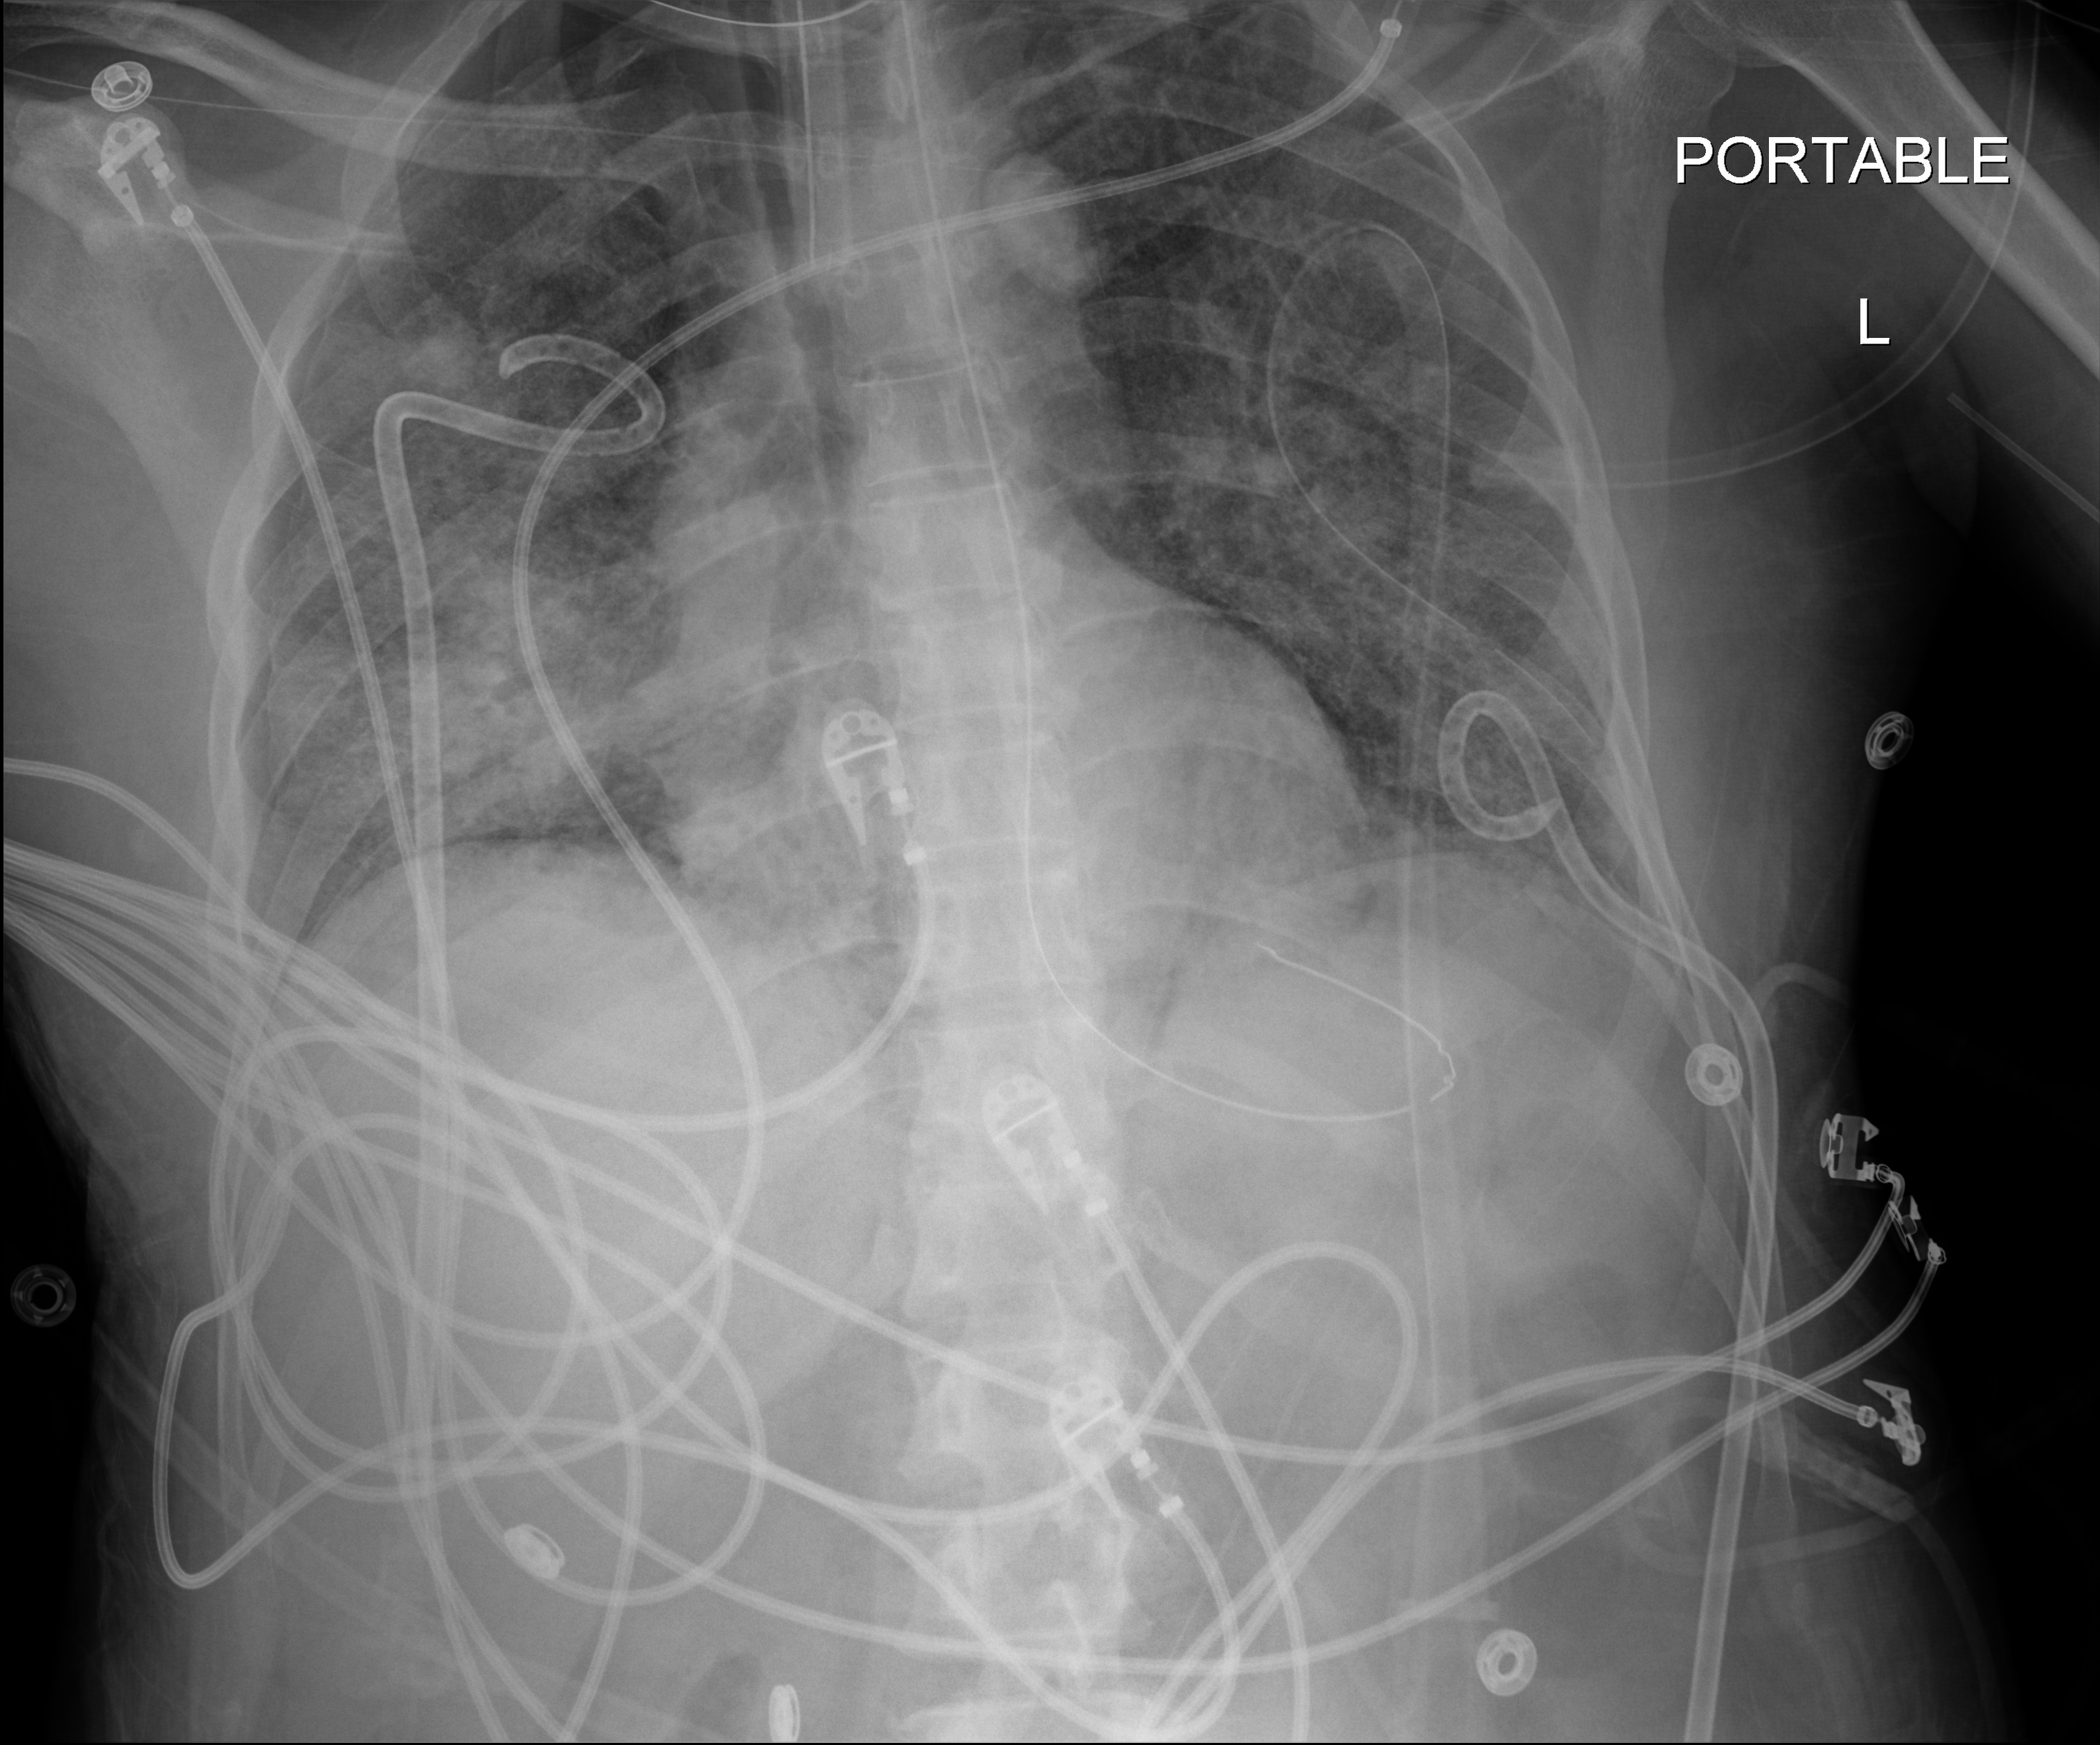
Chest radiograph (digital radiography). Patient hospitalised with COVID-19, aged 18–59 years.
Hospital-stay facts (about this admission, not read from this image; timing relative to this image not recorded):
- other chronic lung disease (admission record): no
- chronic kidney disease (admission record): no
- admitted to intensive care during this hospital stay: yes